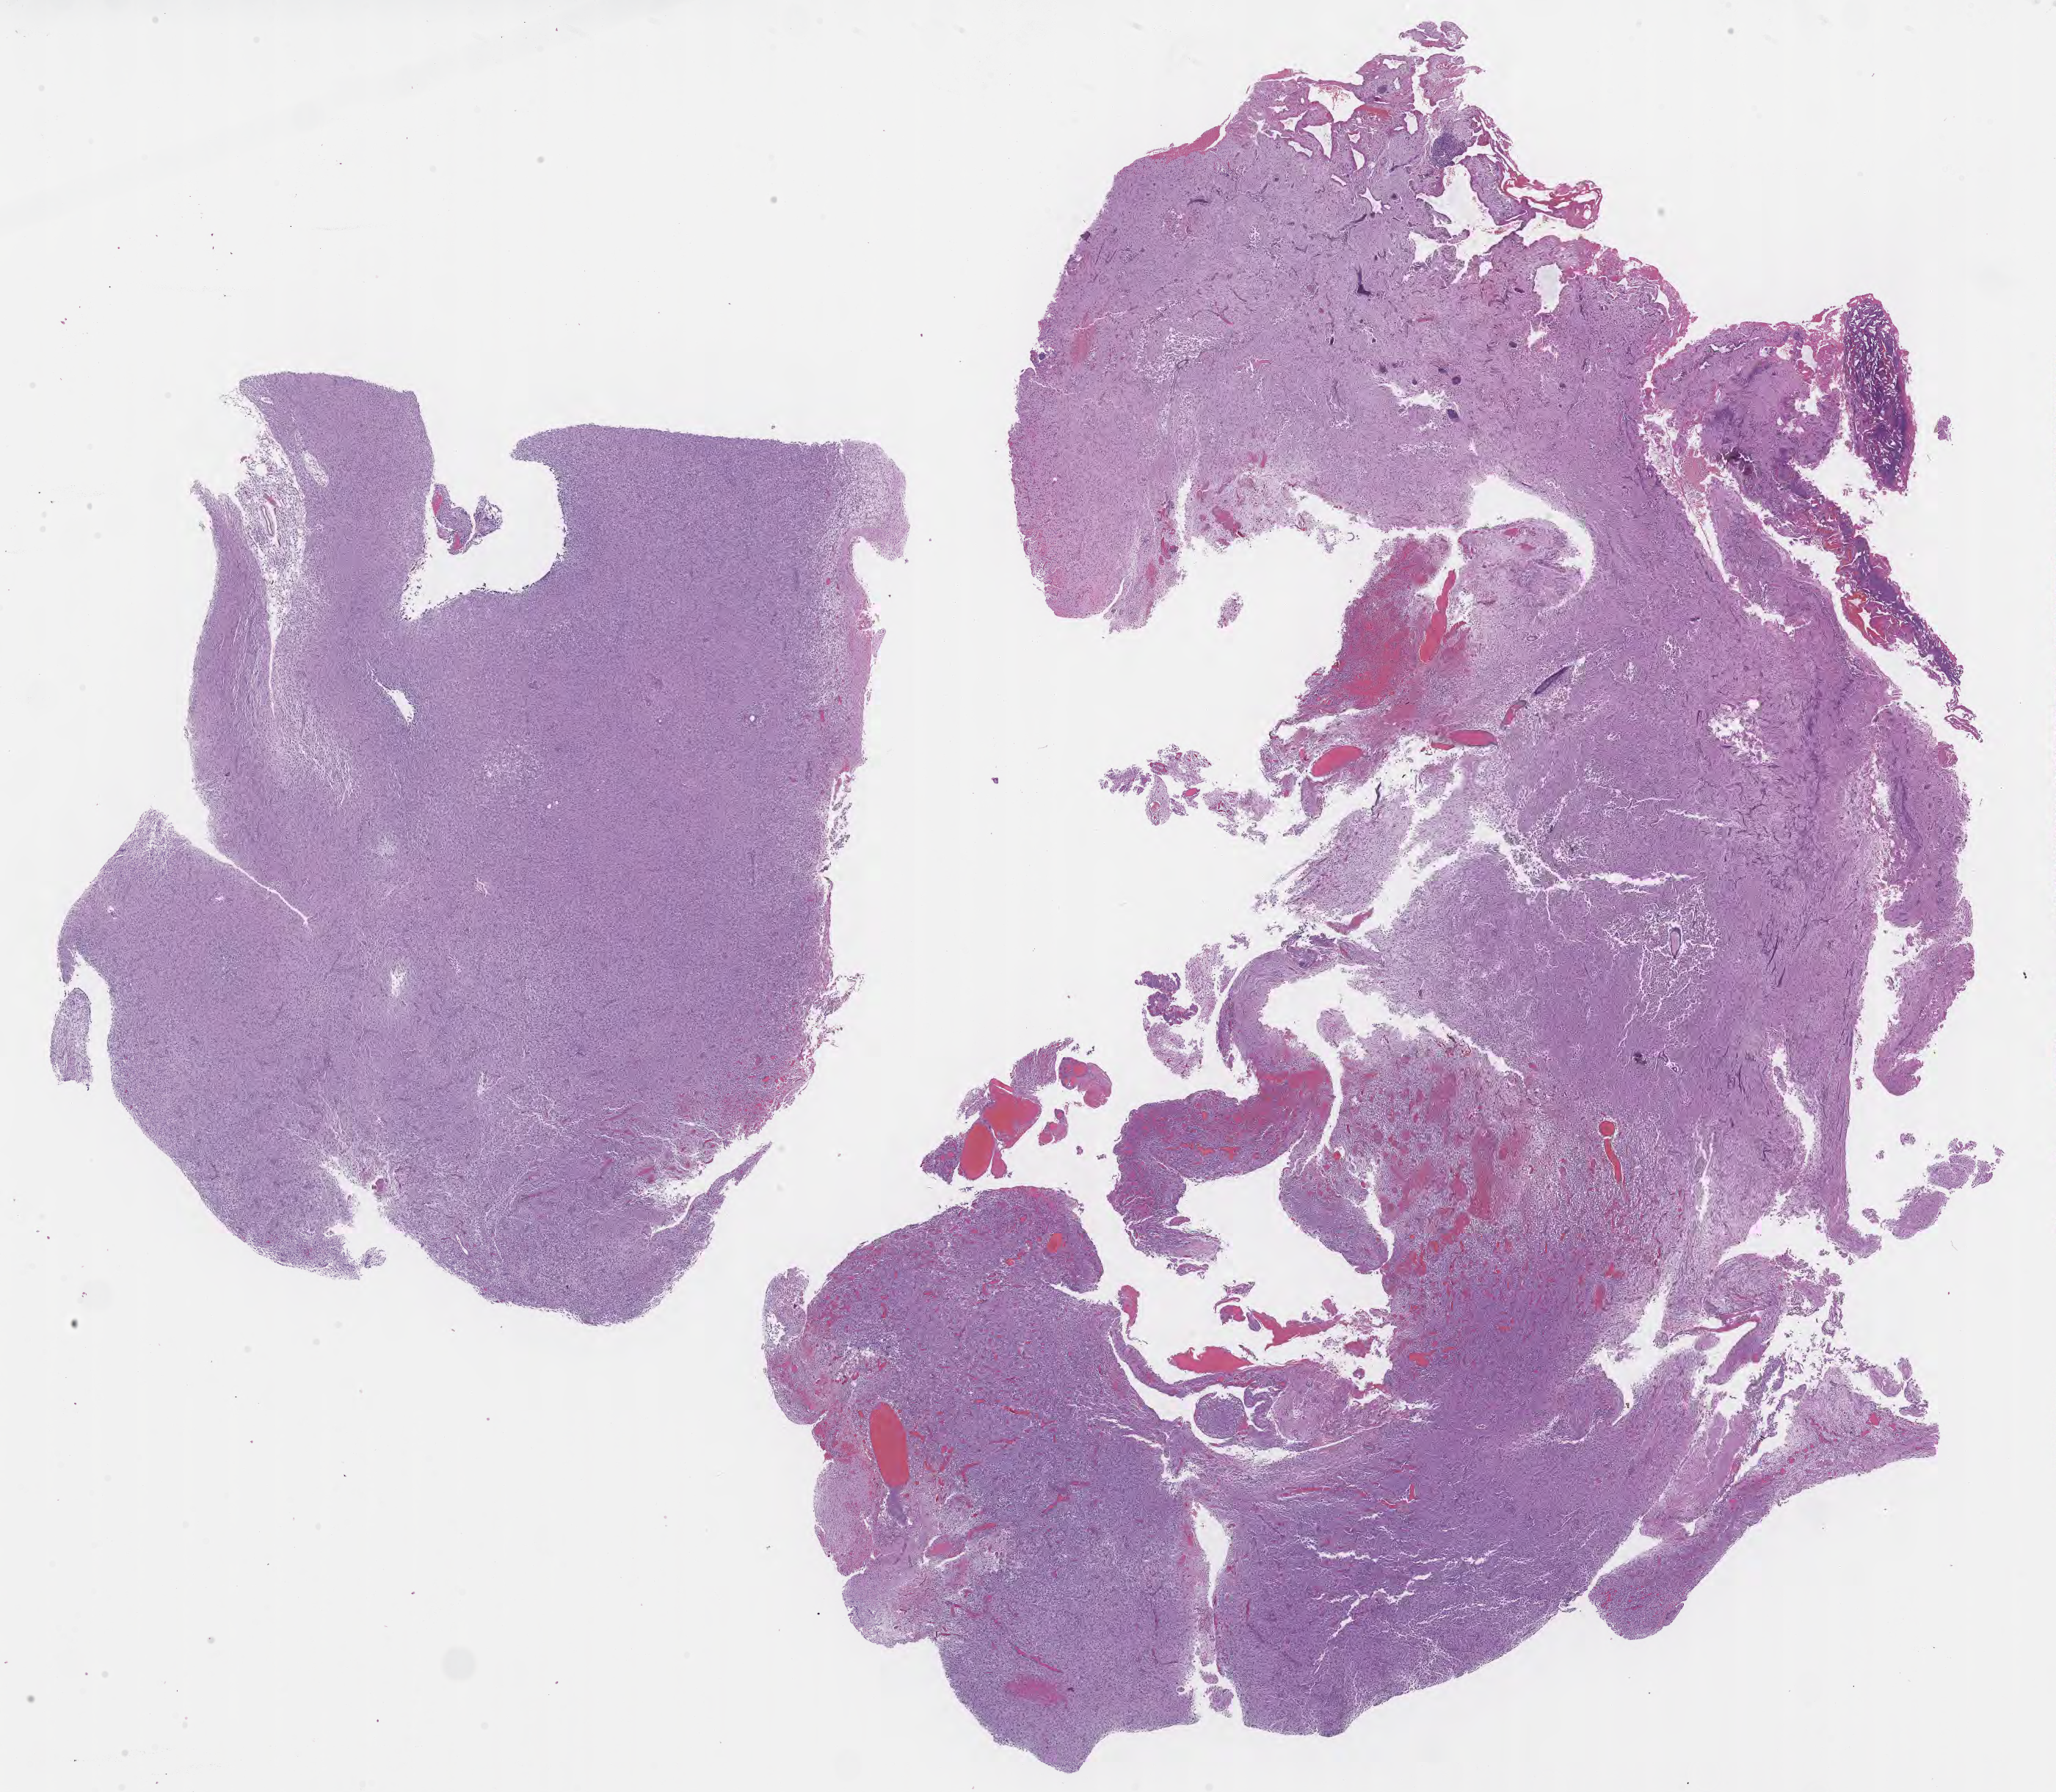
Digitized hematoxylin and eosin (H&E)-stained section of tumor tissue from the temporal lobe — a low-resolution overview of the entire scanned area, about 22.6 x 19.7 mm; formalin-fixed, paraffin-embedded (FFPE) tissue. Male patient, age 306 days.
Recorded diagnosis: Astrocytoma, NOS.